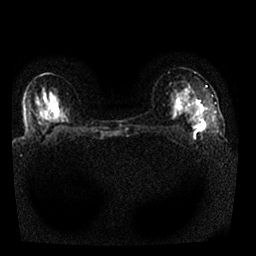
Breast MRI, one axial slice. Slice 16 of 25 in the series (ordered by position). Diffusion-weighted series; image 2 of 4 stored at this slice position (different b-values; order by instance number). 1.5 T. 4 mm slice thickness. 256 × 256 image matrix, field of view 330 × 330 mm. Female patient.
Annotated regions visible in this slice (manually delineated by an expert):
- tumour on diffusion-weighted imaging: bounding box [x1, y1, x2, y2] px = [195, 121, 206, 131]